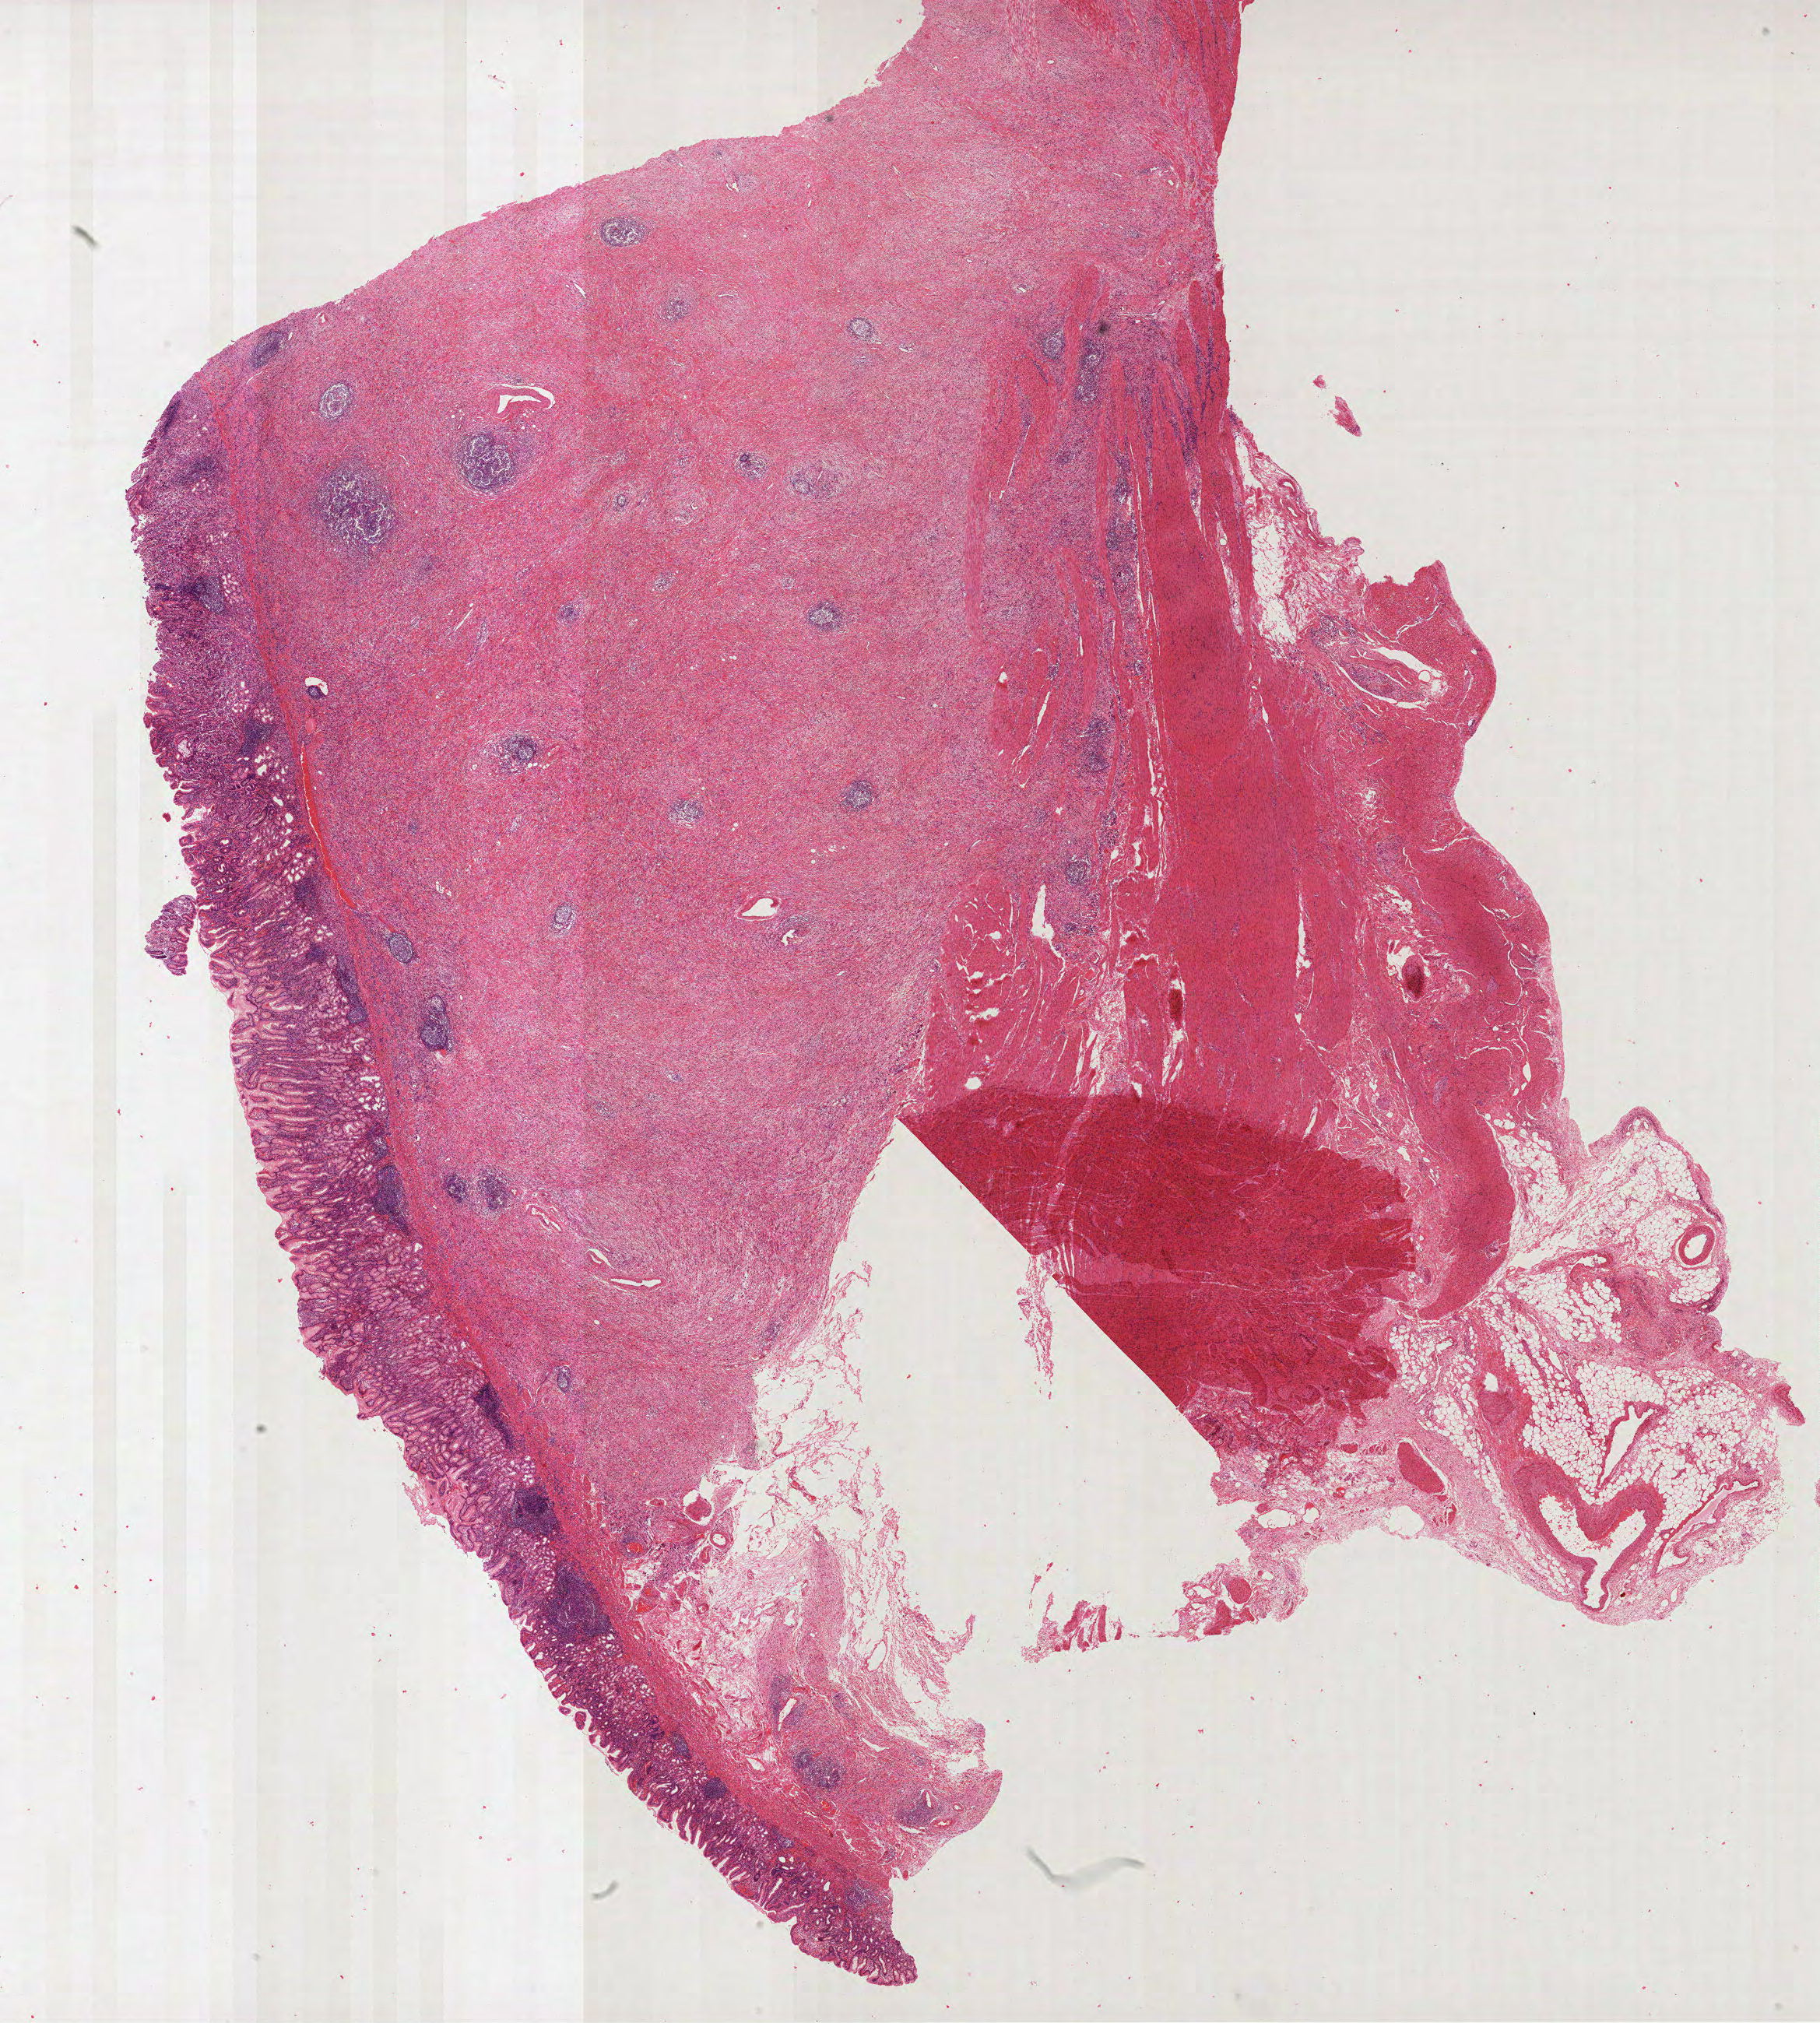
H&E whole-slide image — whole scanned area (about 18.9 x 21.0 mm) shown as a low-resolution overview, formalin-fixed paraffin-embedded (FFPE) diagnostic section, sample: primary tumour, stomach. Patient: male, age at initial diagnosis 69 years. Histologic grade: G3 (poorly differentiated).
Lymph nodes positive (case pathology): 6 of 18 examined. Diagnosis: Adenocarcinoma, NOS (gastric antrum). AJCC pathologic stage: IIIC (7th edition).